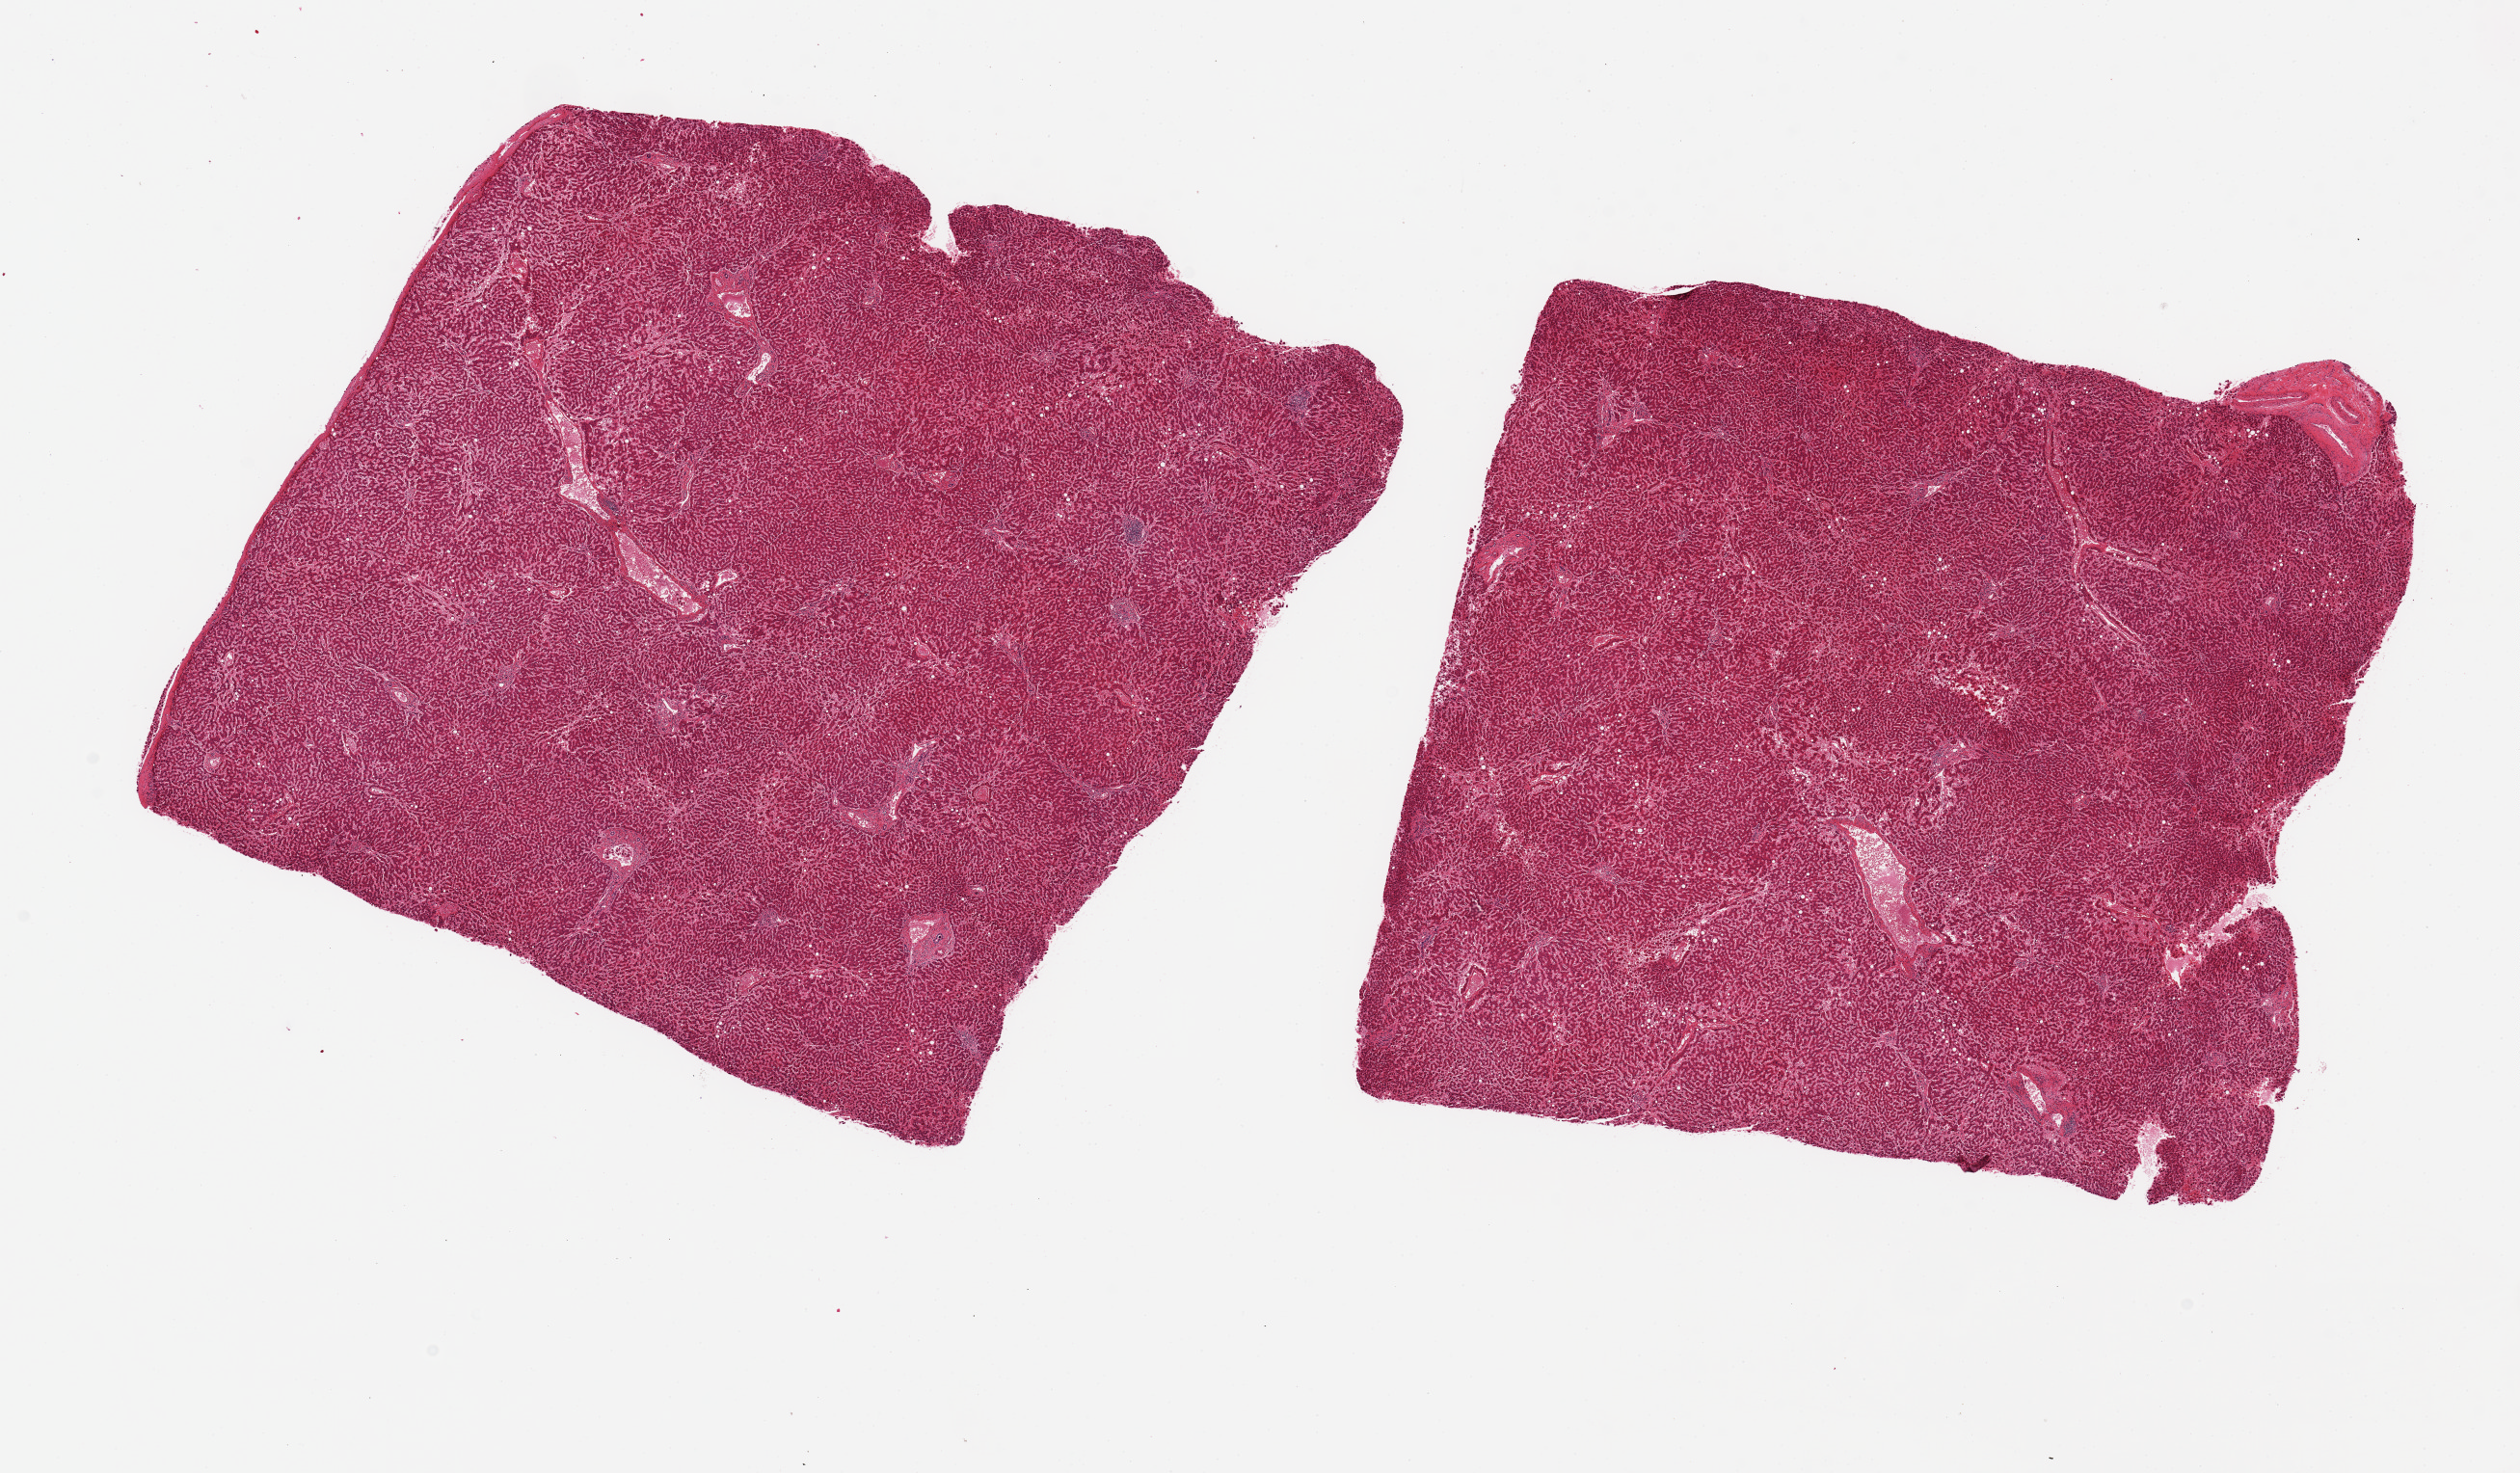
Digitized H&E-stained section — shown as a low-resolution overview of the whole scanned area (about 20.7 x 12.1 mm, from a 20x scan); PAXgene-fixed paraffin-embedded (PFPE) section; section of liver (target tissue); tissue donor sample. Donor: female.
• review note (as recorded): 2 pieces. 8x8 & 8x7mm; moderate central congestion